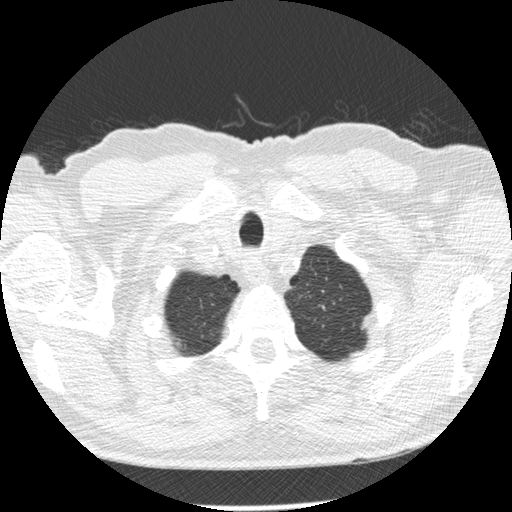
Chest CT (low-dose screening protocol), one axial image, second annual screen, lung window (W 1500 / L -600 HU), 2.5 mm slice thickness, standard (soft-tissue) reconstruction kernel (STANDARD), slice 23 of 276 in the series, 512 × 512 image matrix. Male, age 73 years at enrolment. Former smoker at enrolment.
Lesion marked by an expert reader, box from (x=349, y=304) to (x=390, y=346) px. Screening reader's record for this exam: no non-calcified nodule ≥4 mm recorded. Official screen result: negative screen, minor abnormalities not suspicious for lung cancer.